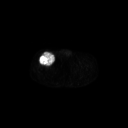
FDG PET of an extremity soft-tissue mass (from a PET/CT study), one axial slice. Position 291 of 311 along the scan axis. 3.27 mm slice thickness. 128 × 128 image matrix, field of view 700 × 700 mm. Patient: male, 56 years. From the clinical record (not read from this slice): histological type: pleiomorphic leiomyosarcoma; grade: intermediate; site of the primary tumour: right thigh.
Structures marked on this image (expert contour drawn on MRI and transferred to this co-registered scan by the dataset authors):
- gross tumour volume including surrounding oedema: box from (x=38, y=52) to (x=55, y=66) px
- gross tumour volume (mass): (x=39, y=52)–(x=55, y=66)